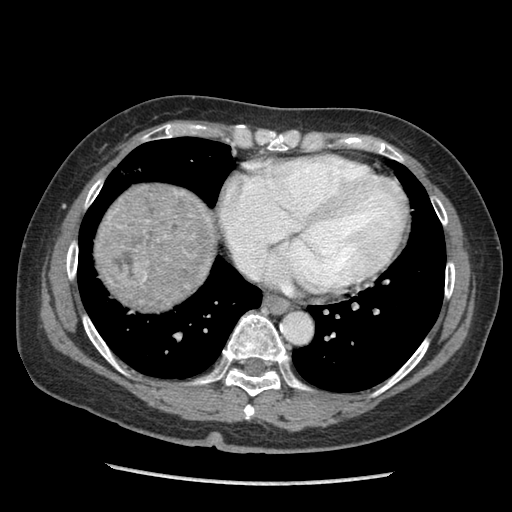
Contrast-enhanced abdominal CT (liver protocol), one axial slice. Slice 92 of 105 in the series (ordered by position). Reconstruction kernel STANDARD. Soft-tissue window (W 400 / L 40 HU). 512 × 512 image matrix, field of view 340 × 340 mm. Case-level facts recorded for this patient, not image findings: diagnosis: hepatocellular carcinoma (patient treated with transarterial chemoembolisation; whether this scan precedes or follows treatment is not stated here); TNM stage (as recorded): Stage-I; Child-Pugh class: A; tumour differentiation: moderately differentiated; tumour nodularity: uninodular.
Outlined on this slice (semi-automatic segmentation, software-assisted and operator-edited):
- liver parenchyma outside the tumour (the mass and vessels are separate outlines, so this box may not span the whole liver): box from (x=96, y=182) to (x=212, y=308) px
- mass: (x=98, y=185)–(x=218, y=311)